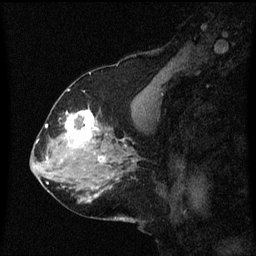
Breast MRI (dynamic contrast-enhanced), one sagittal slice; slice 29 of 60 in the series (ordered by position); dynamic contrast-enhanced series, image 2 of 3 at this slice position (ordered by acquisition); 1.5 T; TE 4.2 ms, TR 8.4 ms; 2 mm slice thickness; 256 × 256 image matrix, field of view 200 × 200 mm. Patient: female, 58 years.
Annotated regions visible in this slice (semi-automatic segmentation, software-assisted and operator-edited):
- analysis volume of interest (the breast-tissue region the enhancement analysis was run in; not a lesion): bounding box [x1, y1, x2, y2] px = [58, 104, 99, 151]
- tumour enhancement mask (voxels above the 70 % enhancement threshold inside the analysis volume of interest): [66, 110, 99, 149]